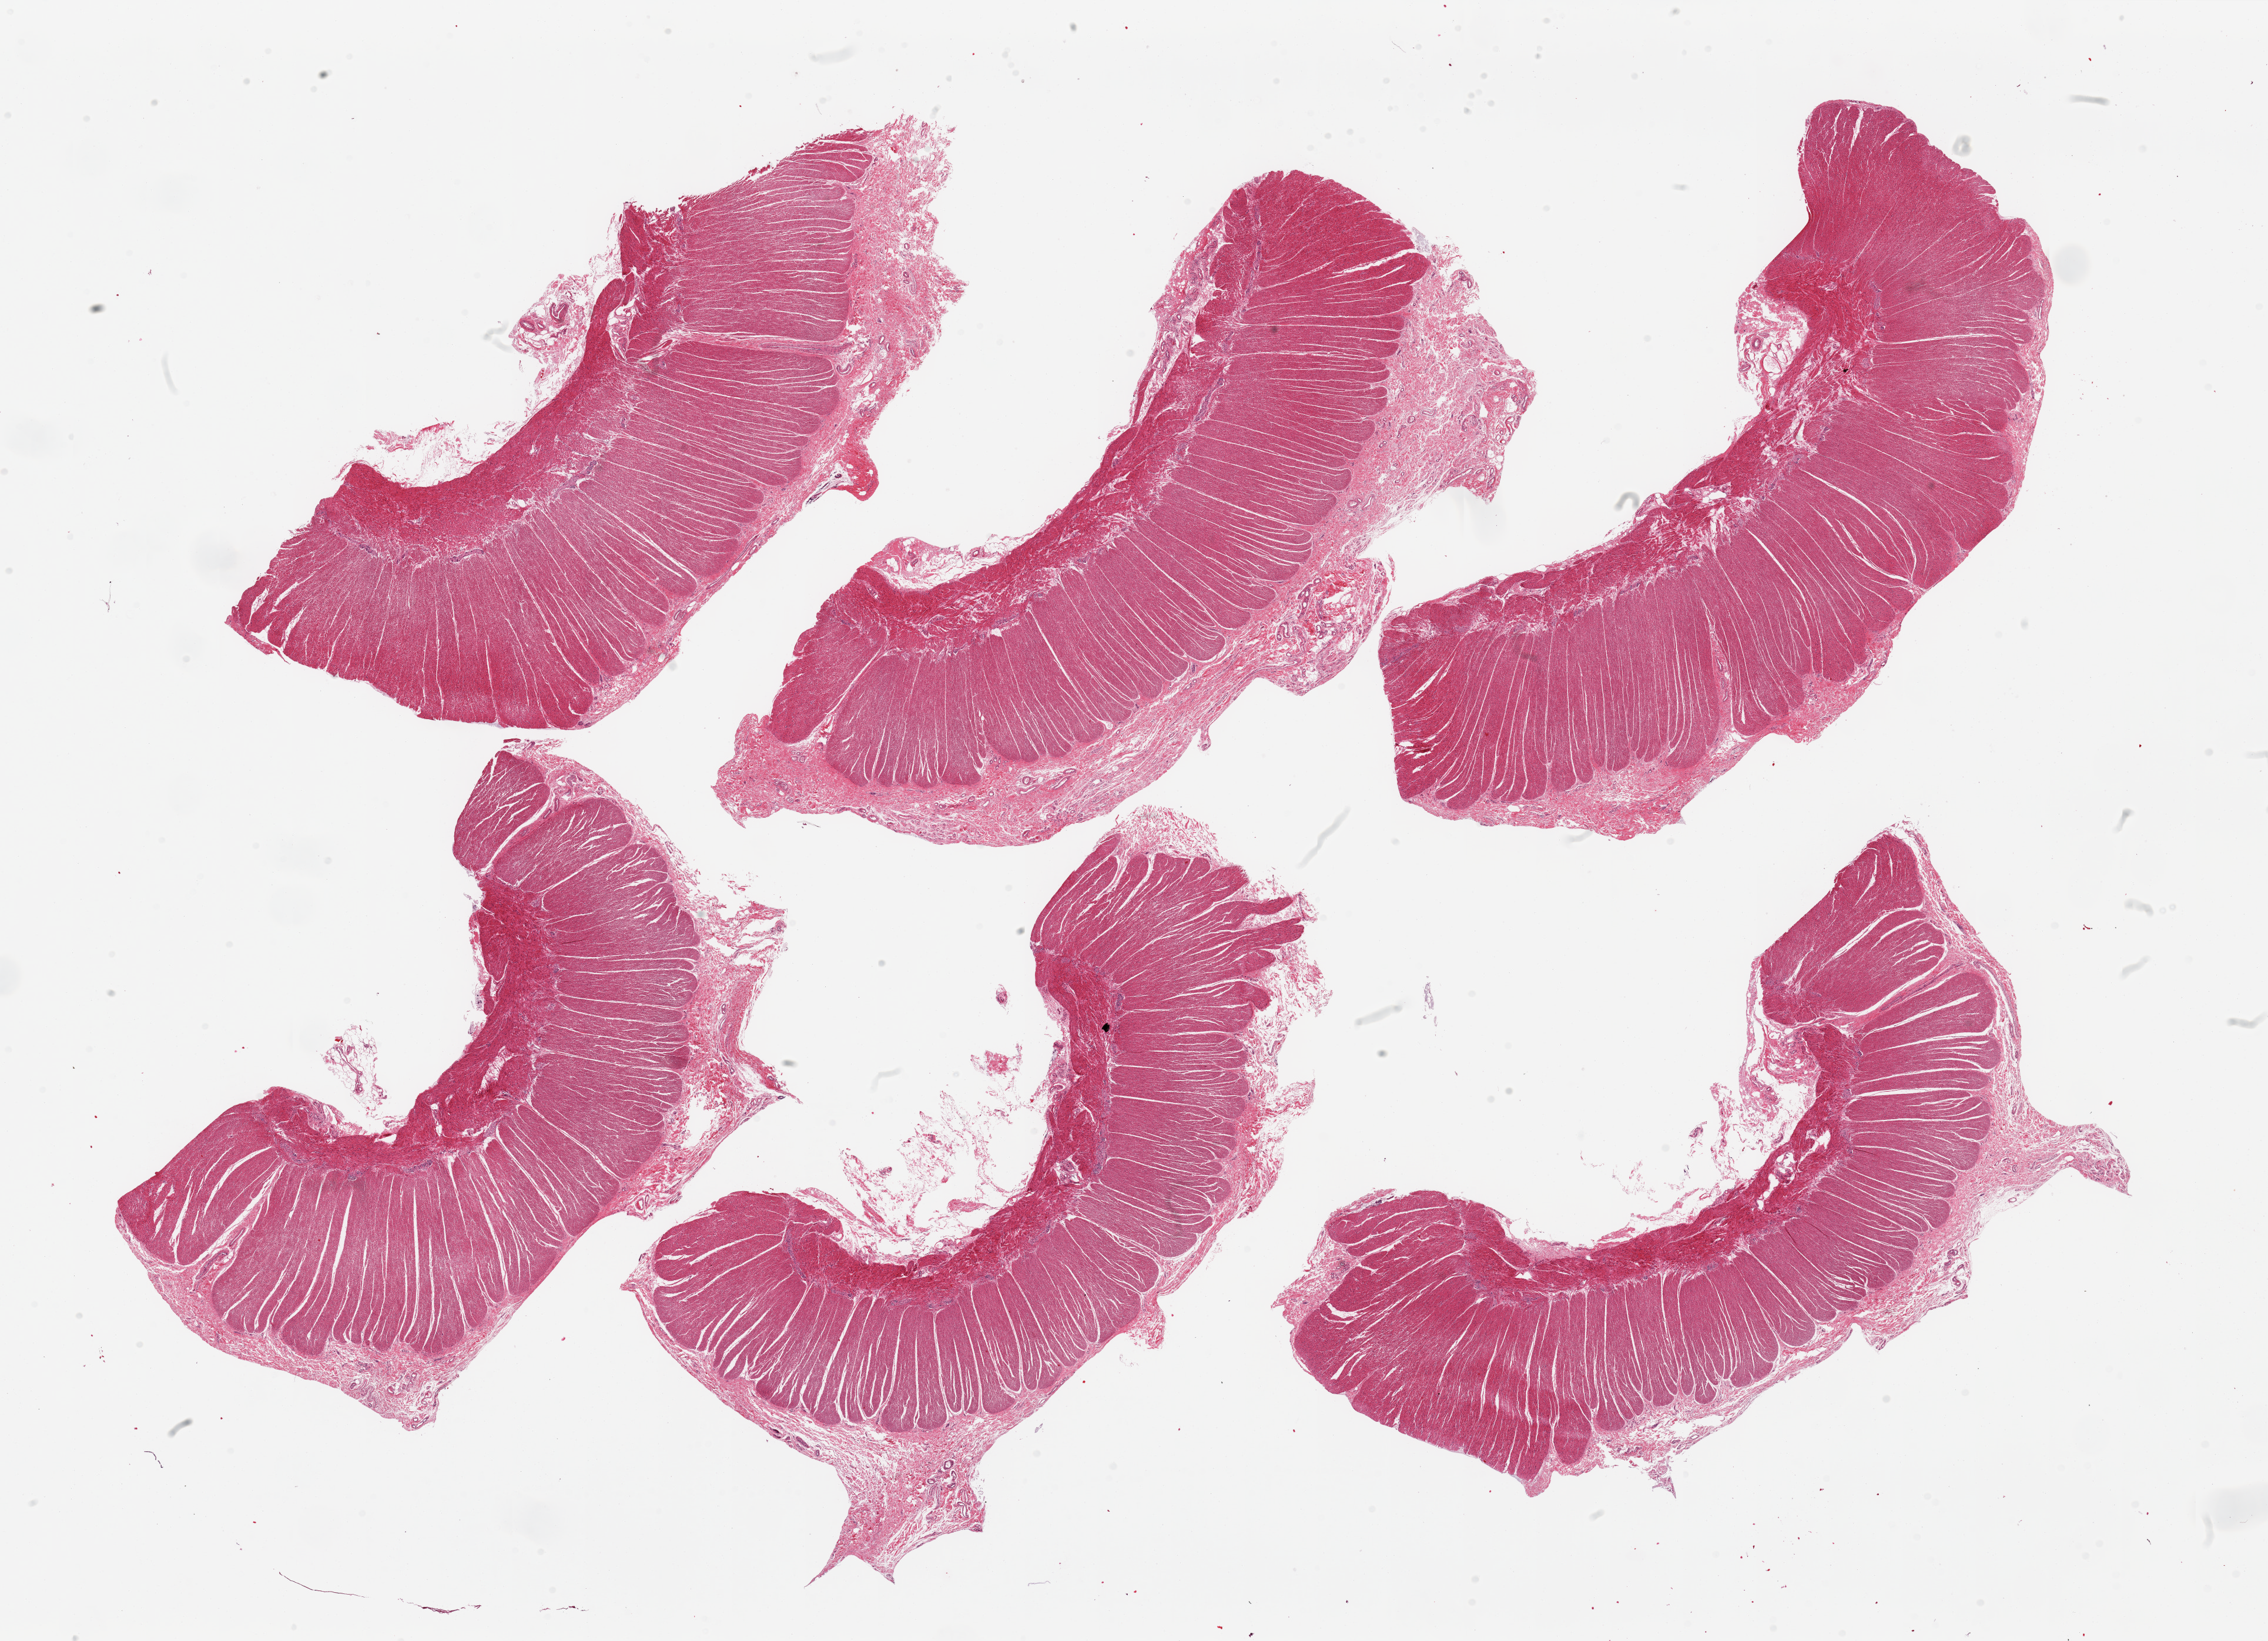
H&E whole-slide image, brightfield, shown as a low-resolution overview of the whole scanned area (about 30.5 x 22.1 mm); PAXgene-fixed paraffin-embedded (PFPE) section; section of sigmoid colon (target tissue); tissue donor sample.
Reviewer comment on this tissue sample: 6 pieces, confirmed target muscularis.